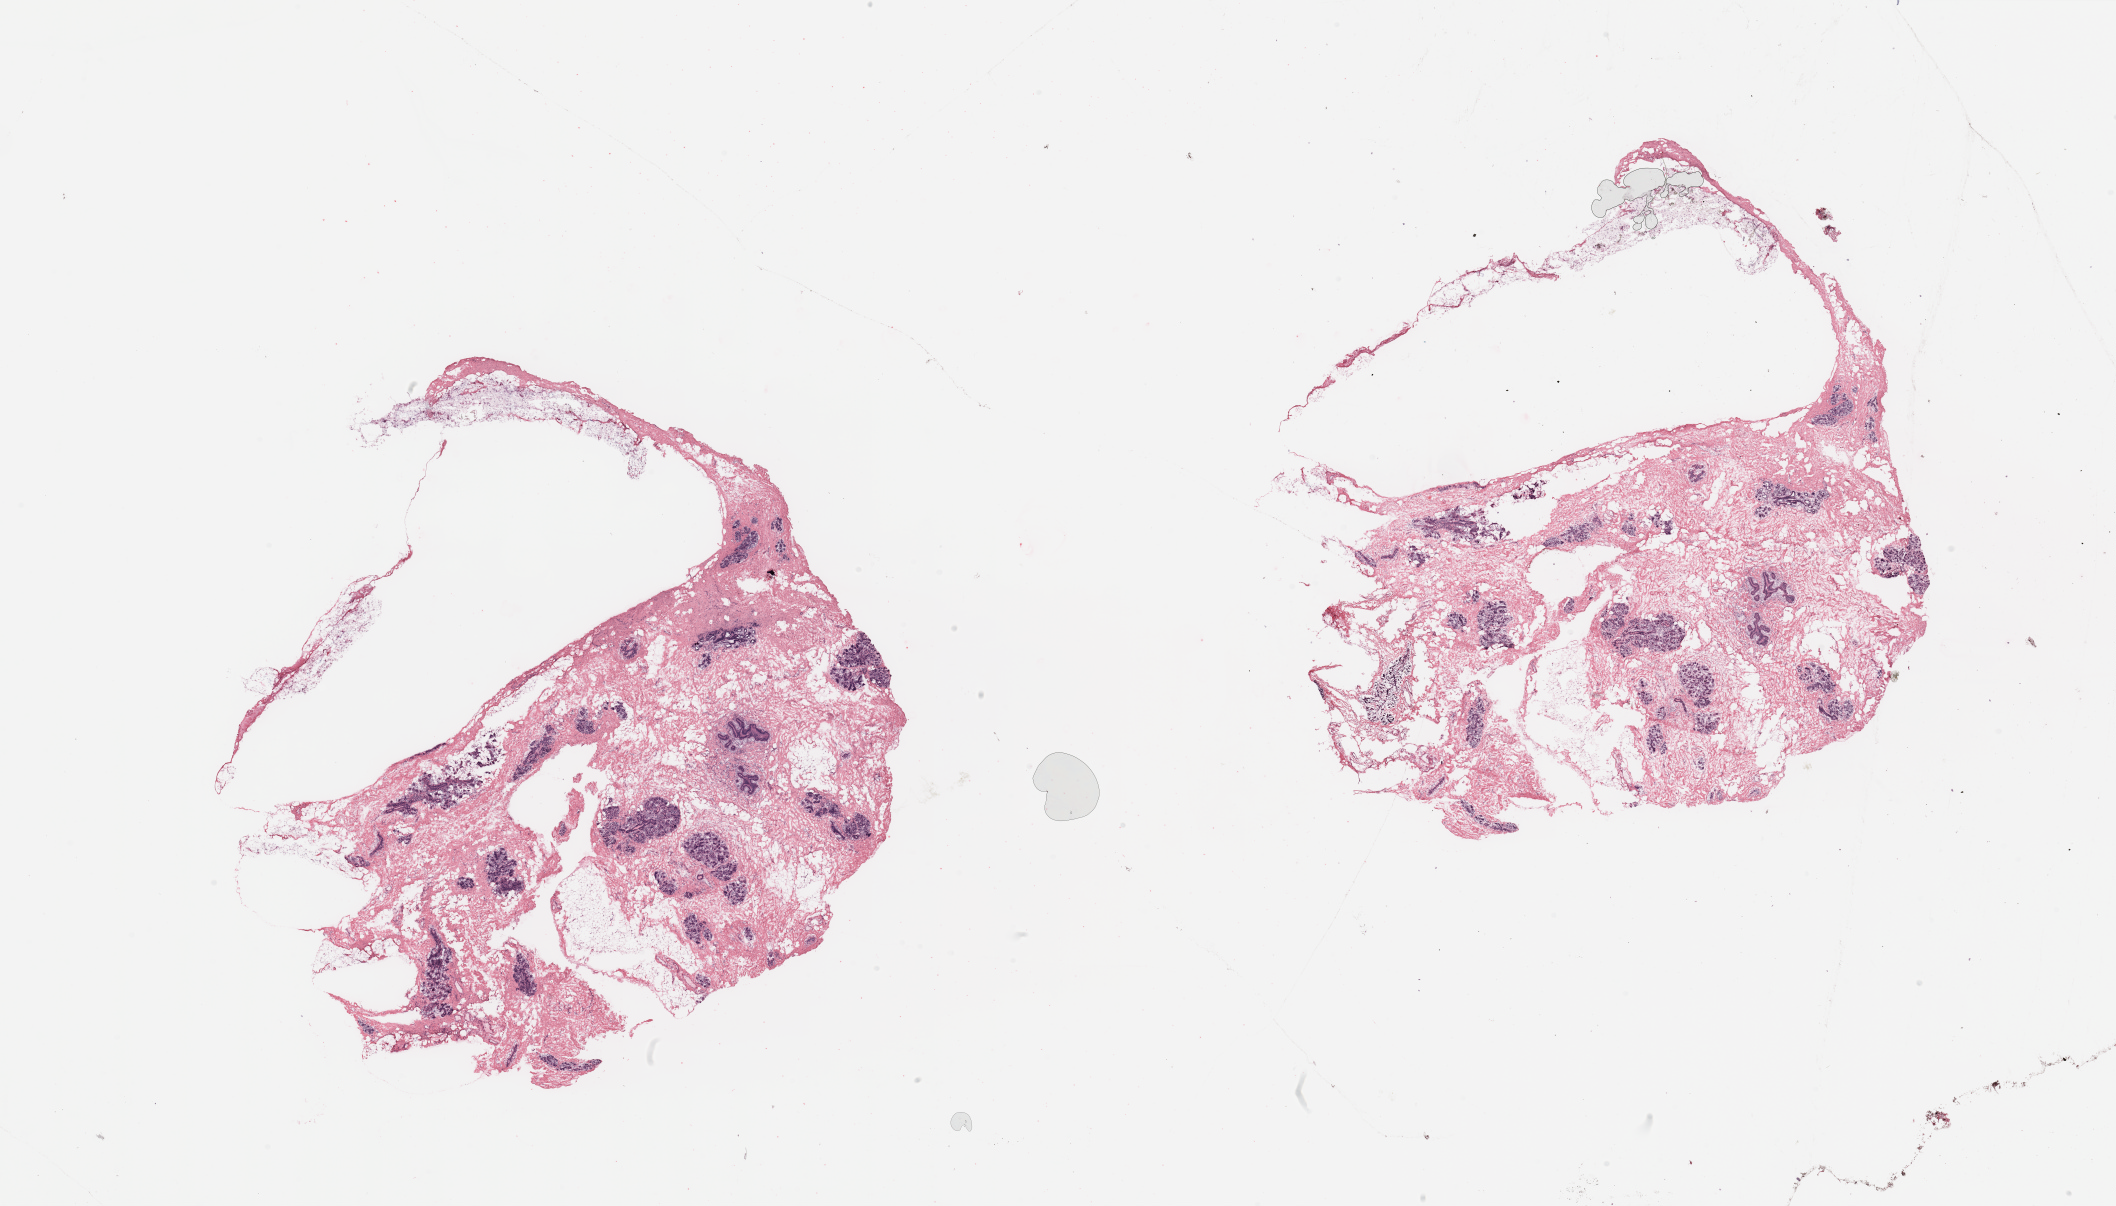
H&E-stained whole-slide image, a low-resolution overview of the entire scanned area, about 33.5 x 19.1 mm, breast, tumour tissue. Patient: female, age 55 years.
* histologic diagnosis: Infiltrating duct carcinoma, NOS
* AJCC pathologic stage: IIA